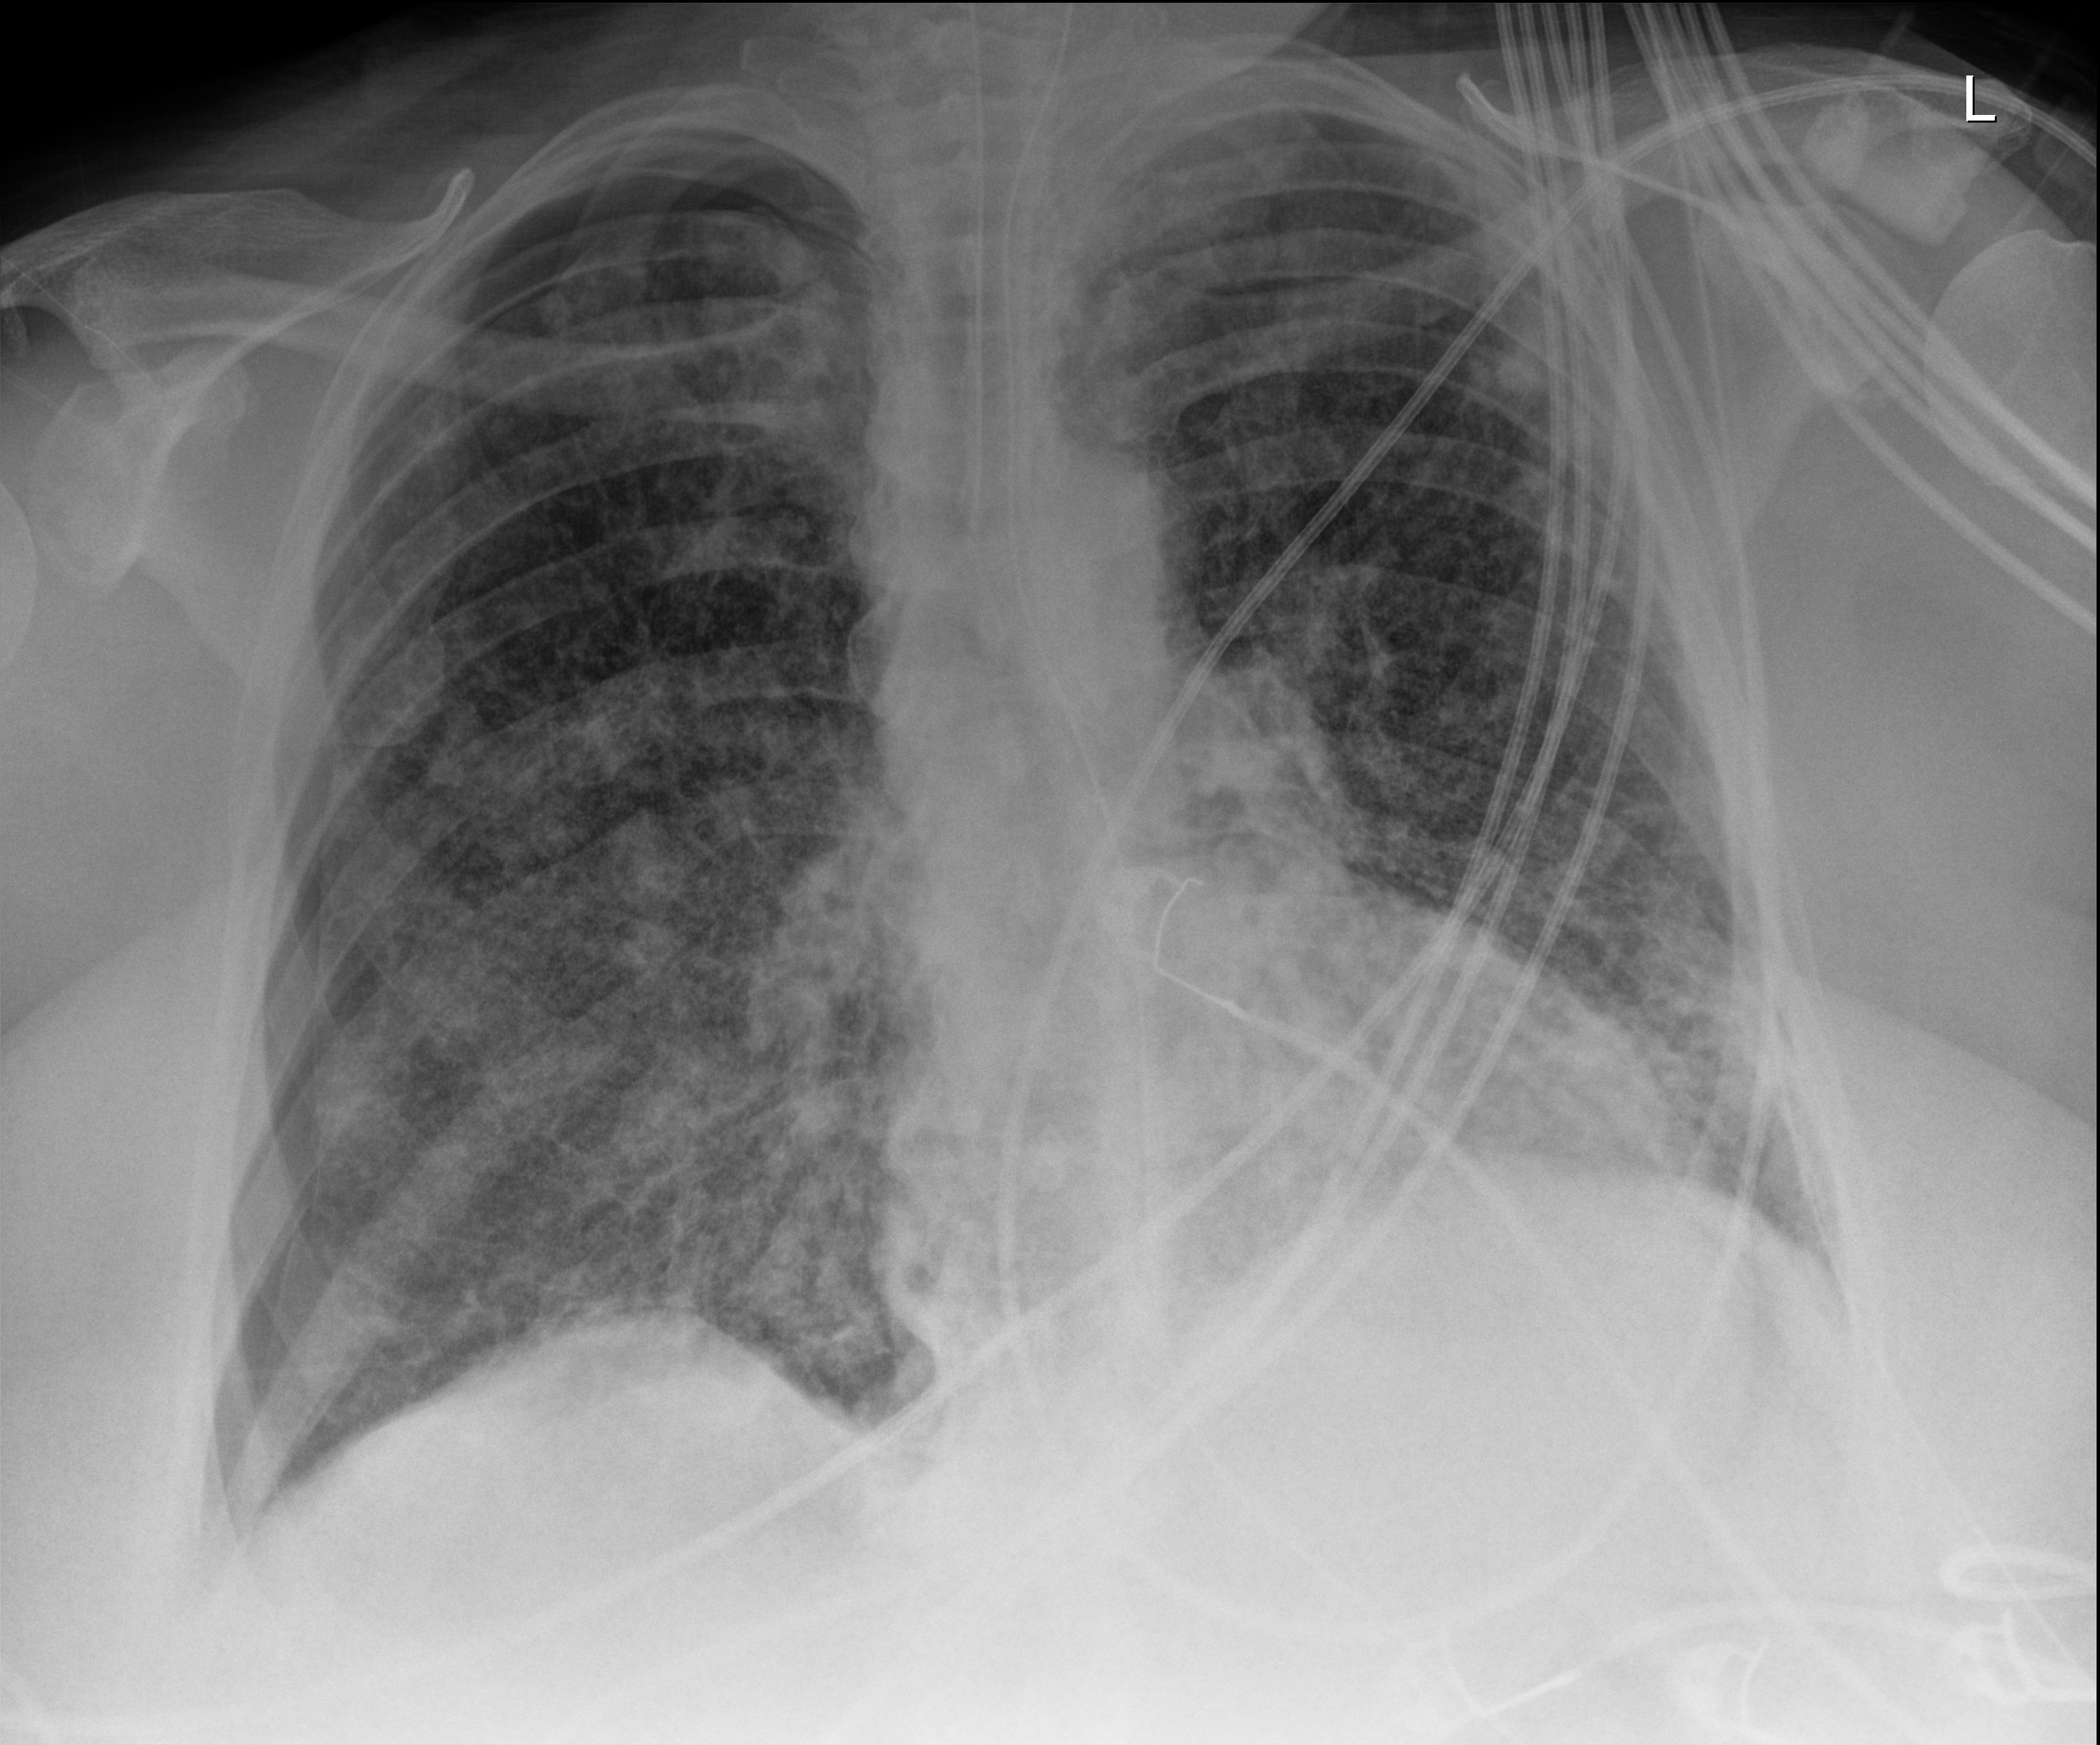
Portable chest radiograph; anteroposterior (AP) projection. Patient hospitalised with COVID-19, aged 18–59 years.
From the hospital-stay record, not from the radiograph (when in the stay this image was taken is not recorded):
- mechanically ventilated during this hospital stay: yes